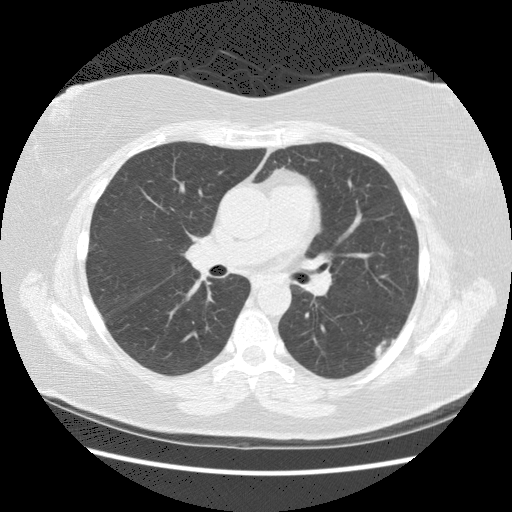
Chest CT (low-dose screening protocol), one axial image; second annual screen; lung window (W 1500 / L -600 HU); 2.5 mm slice thickness; slice 79 of 140 in the series; 512 × 512 image matrix, field of view 360 × 360 mm. Female participant, aged 57 years at enrolment.
Lesion marked by an expert reader, bounding box [x1, y1, x2, y2] px = [361, 329, 401, 368]. Screening reader's record for this exam (one nodule recorded; not confirmed to be the boxed lesion): non-calcified nodule or mass ≥4 mm, left lower lobe, 19 × 9 mm, poorly defined margins, mixed attenuation, pre-existing on the prior screen: yes; interval growth: yes. Participant outcome: lung cancer diagnosed 560 days after this screen (after the third annual screen) — squamous cell carcinoma, NOS, left lower lobe, poorly differentiated (G3), stage IB (AJCC 6th edition), 40 mm at pathology.